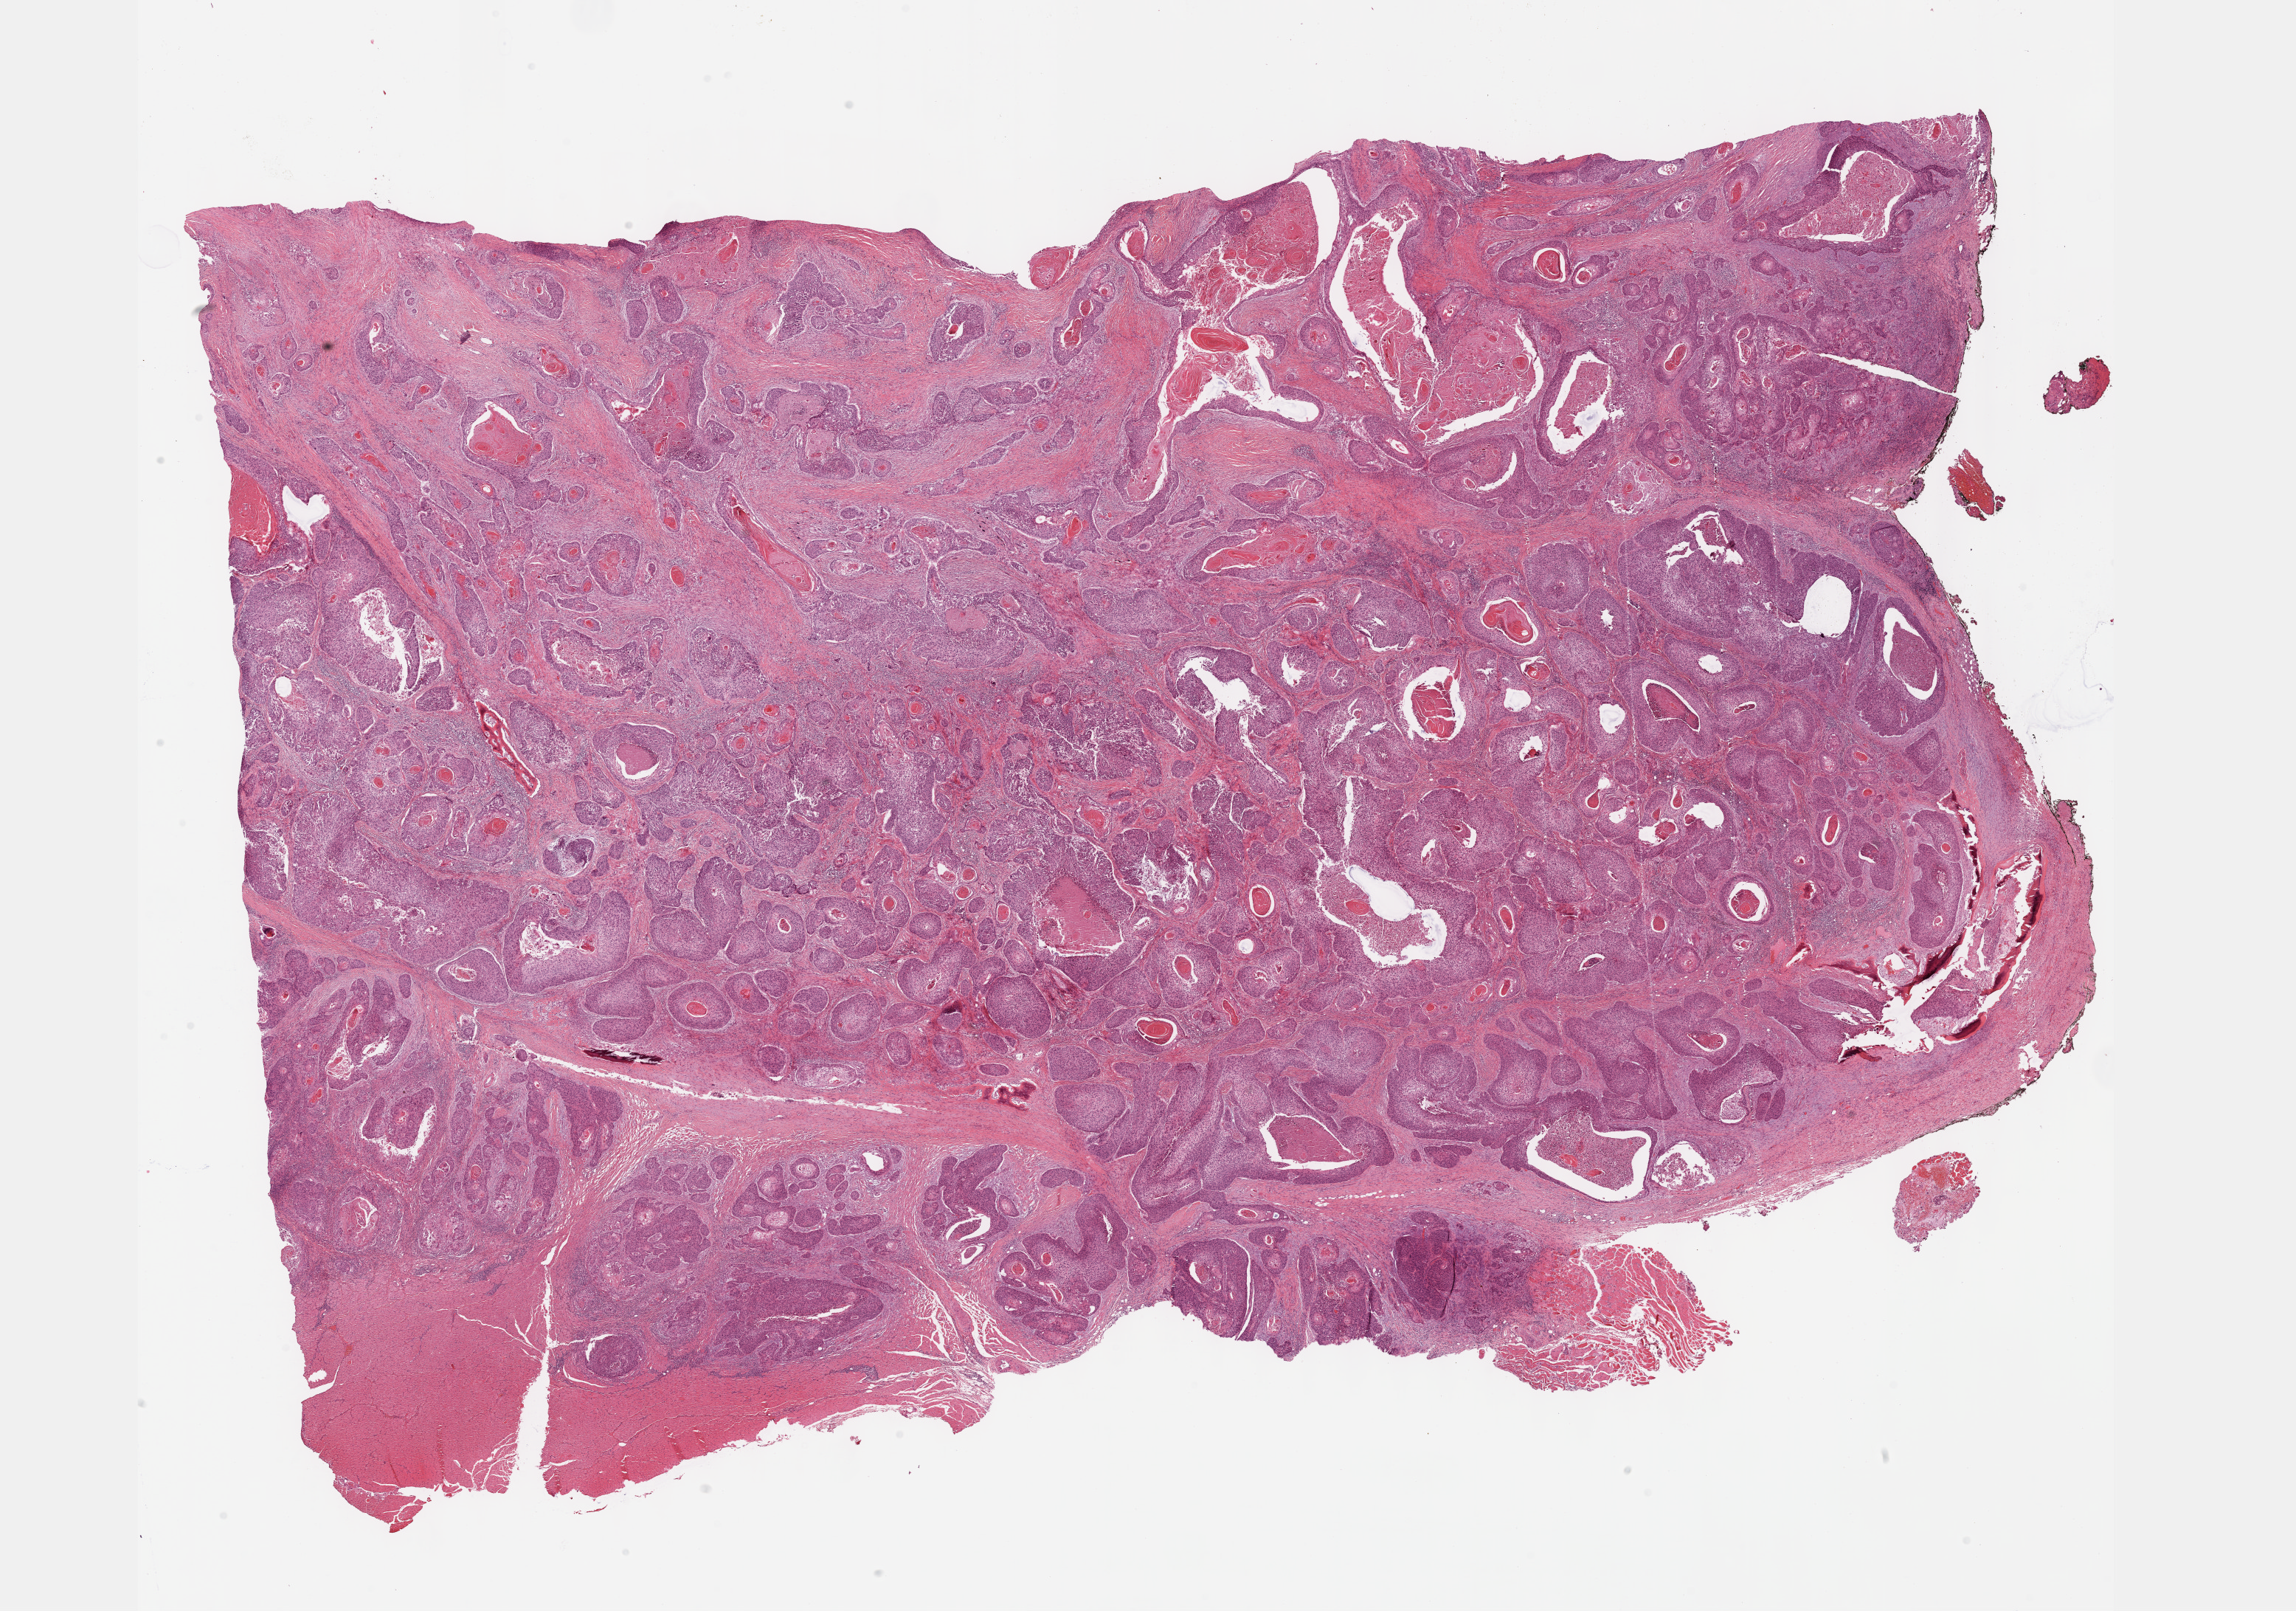
H&E whole-slide image, shown as a low-resolution overview of the whole scanned area (about 25.1 x 17.6 mm), FFPE section, head and neck, primary tumour sample. Male patient; age at initial diagnosis 80 years. Histologic grade: G2 (moderately differentiated).
AJCC pathologic stage: IVA (7th edition). Pathologic diagnosis: Squamous cell carcinoma, NOS (larynx, NOS). Laterality: left.